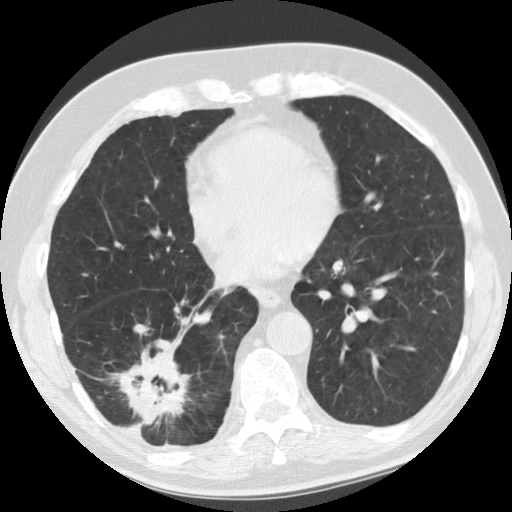
Low-dose screening chest CT, one axial slice; position 48 of 135 along the scan axis; lung window (W 1500 / L -600 HU); 2.5 mm slice thickness; 512 × 512 image matrix, field of view 340 × 340 mm.
Structures marked on this image (outlined manually by an expert reader):
- lesion 1 (tumor, lower lobe of right lung): box from (x=116, y=339) to (x=190, y=426) px